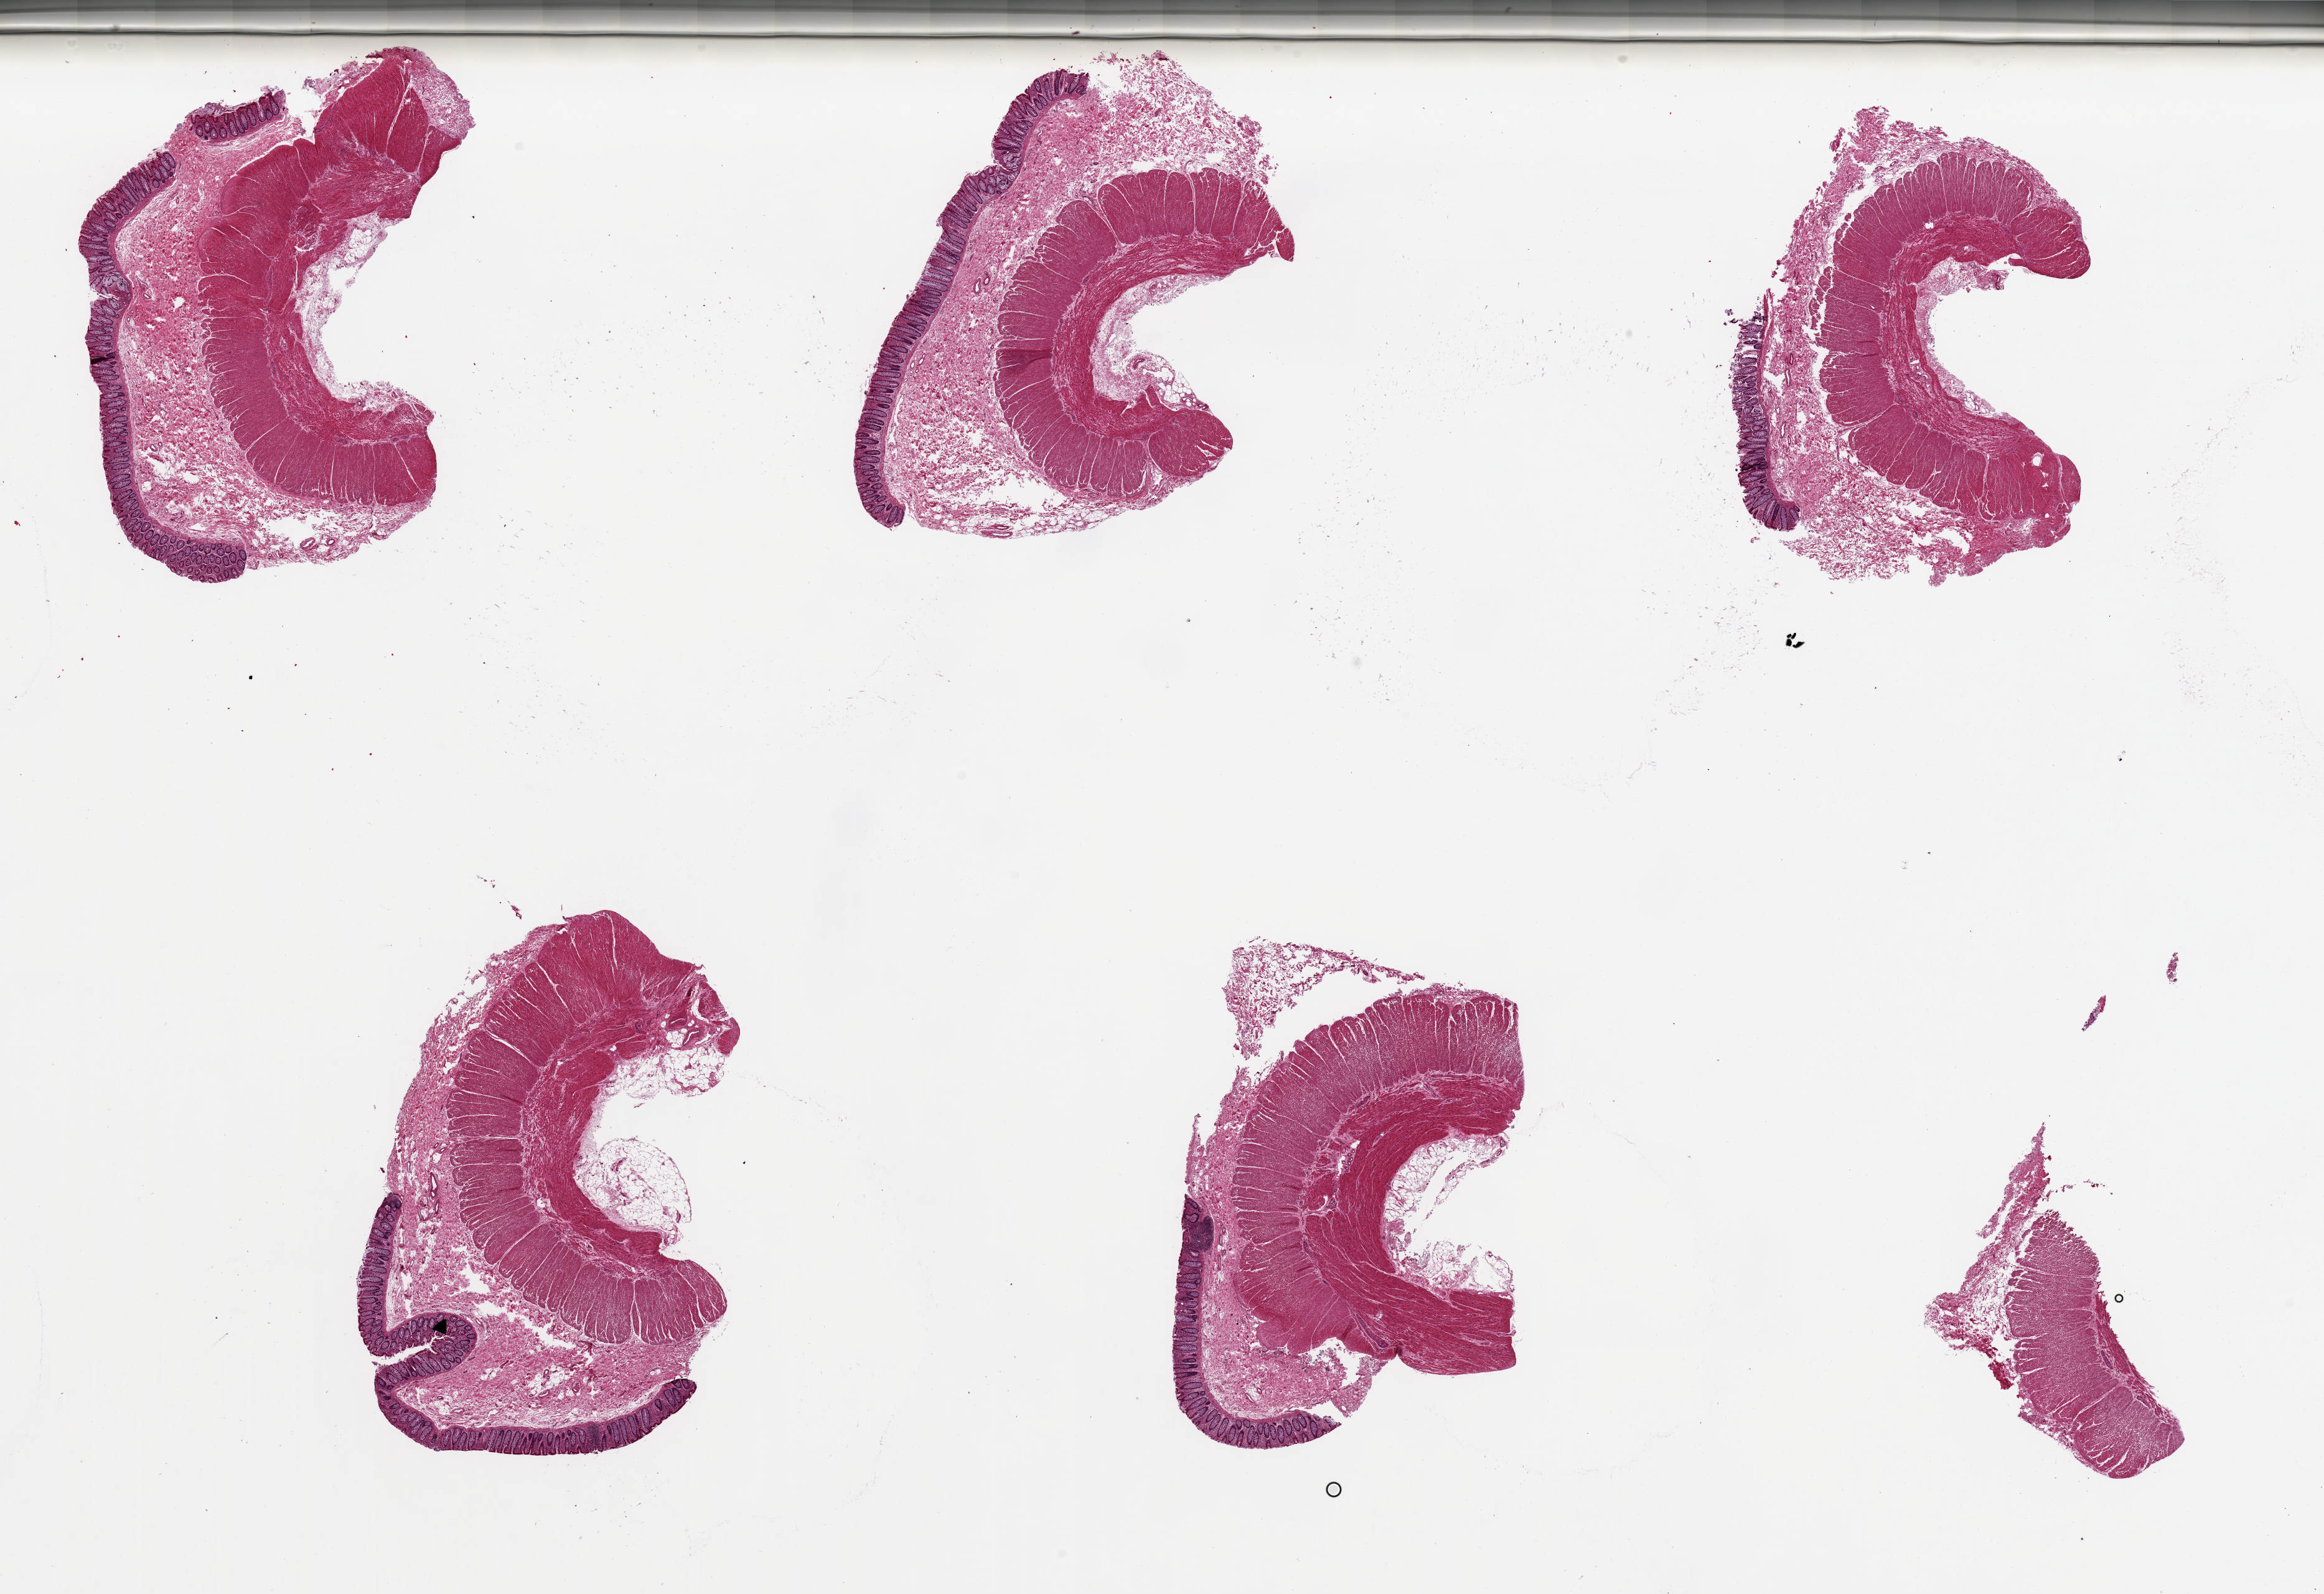
Hematoxylin and eosin (H&E) whole-slide image, low-resolution overview of the scanned area, about 29.5 x 20.3 mm (slide scanned at 20x); PAXgene-fixed, paraffin-embedded tissue; sampled site (target tissue): transverse colon; donor tissue sample. Donor sex: male.
• reviewer comment on this tissue sample: 6 pieces ~6x4mm, 5 with mucosa, well preserved, up to 15% thickness